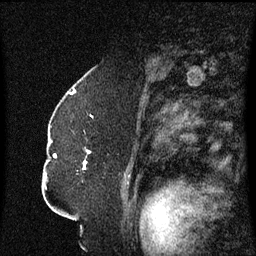
Breast MRI (dynamic contrast-enhanced), one sagittal slice. Position 43 of 60 along the scan axis. Dynamic contrast-enhanced series, image 2 of 3 at this slice position (ordered by acquisition). 1.5 T. TE 4.2 ms, TR 8.4 ms. 2.3 mm slice thickness. 256 × 256 image matrix, field of view 200 × 200 mm. Patient: female, 52 years. Case-level facts recorded for this patient, not image findings: setting: breast cancer imaged before/during neoadjuvant chemotherapy; receptor status: HR-positive, HER2-negative.
Structures marked on this image (semi-automatic segmentation, software-assisted and operator-edited):
- analysis volume of interest (the breast-tissue region the enhancement analysis was run in; not a lesion): bounding box [x1, y1, x2, y2] px = [49, 124, 125, 187]
- tumour enhancement mask (voxels above the 70 % enhancement threshold inside the analysis volume of interest): [54, 152, 91, 169]